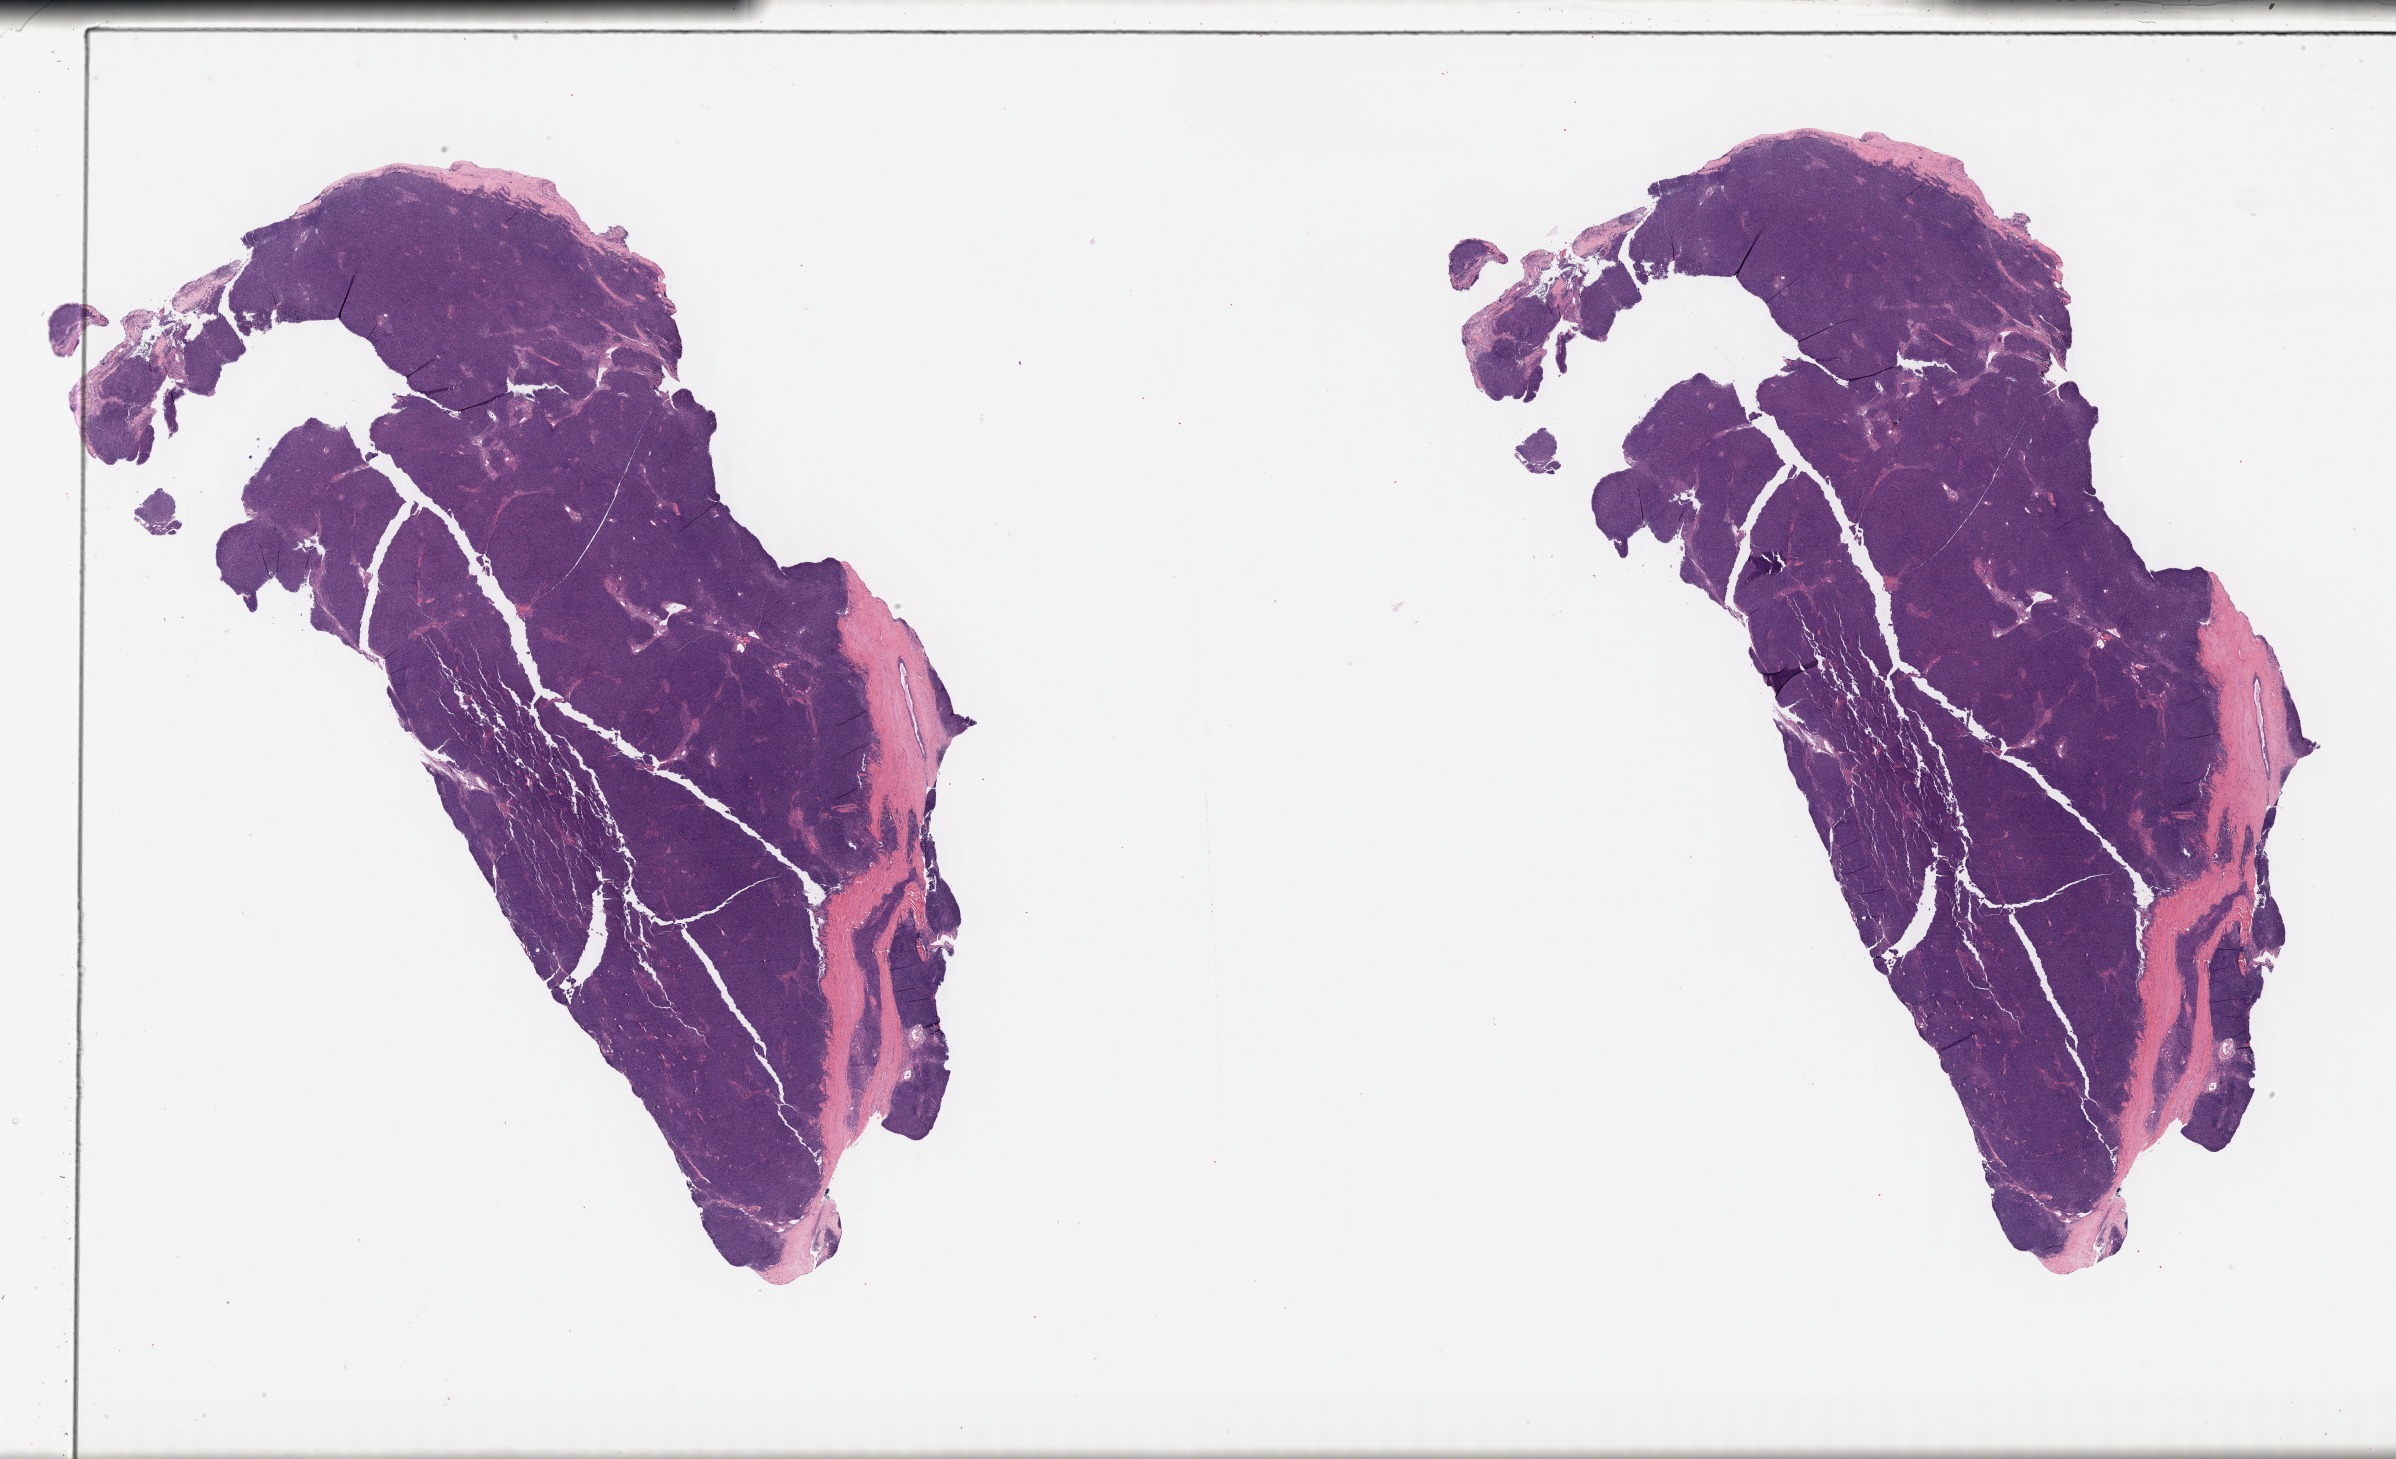
Whole-slide histology image, Hematoxylin and eosin (H&E) stained — a low-resolution overview of the entire scanned area, about 38.8 x 23.6 mm, formalin-fixed paraffin-embedded (FFPE) diagnostic section, primary tumour sample from the thymus. Male patient; age at initial diagnosis 68 years.
• histologic diagnosis: Thymoma, type AB, malignant